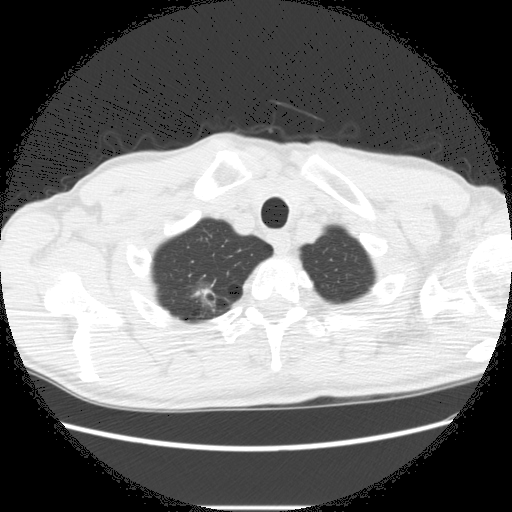
Low-dose screening chest CT, one axial slice; position 261 of 282 along the scan axis; reconstruction kernel STANDARD; 120 kVp; lung window (W 1500 / L -600 HU); 2.5 mm slice thickness; 512 × 512 image matrix.
Outlined on this slice (manually delineated by an expert):
- lesion 2 (nodule, upper lobe of right lung): box from (x=192, y=288) to (x=218, y=308) px